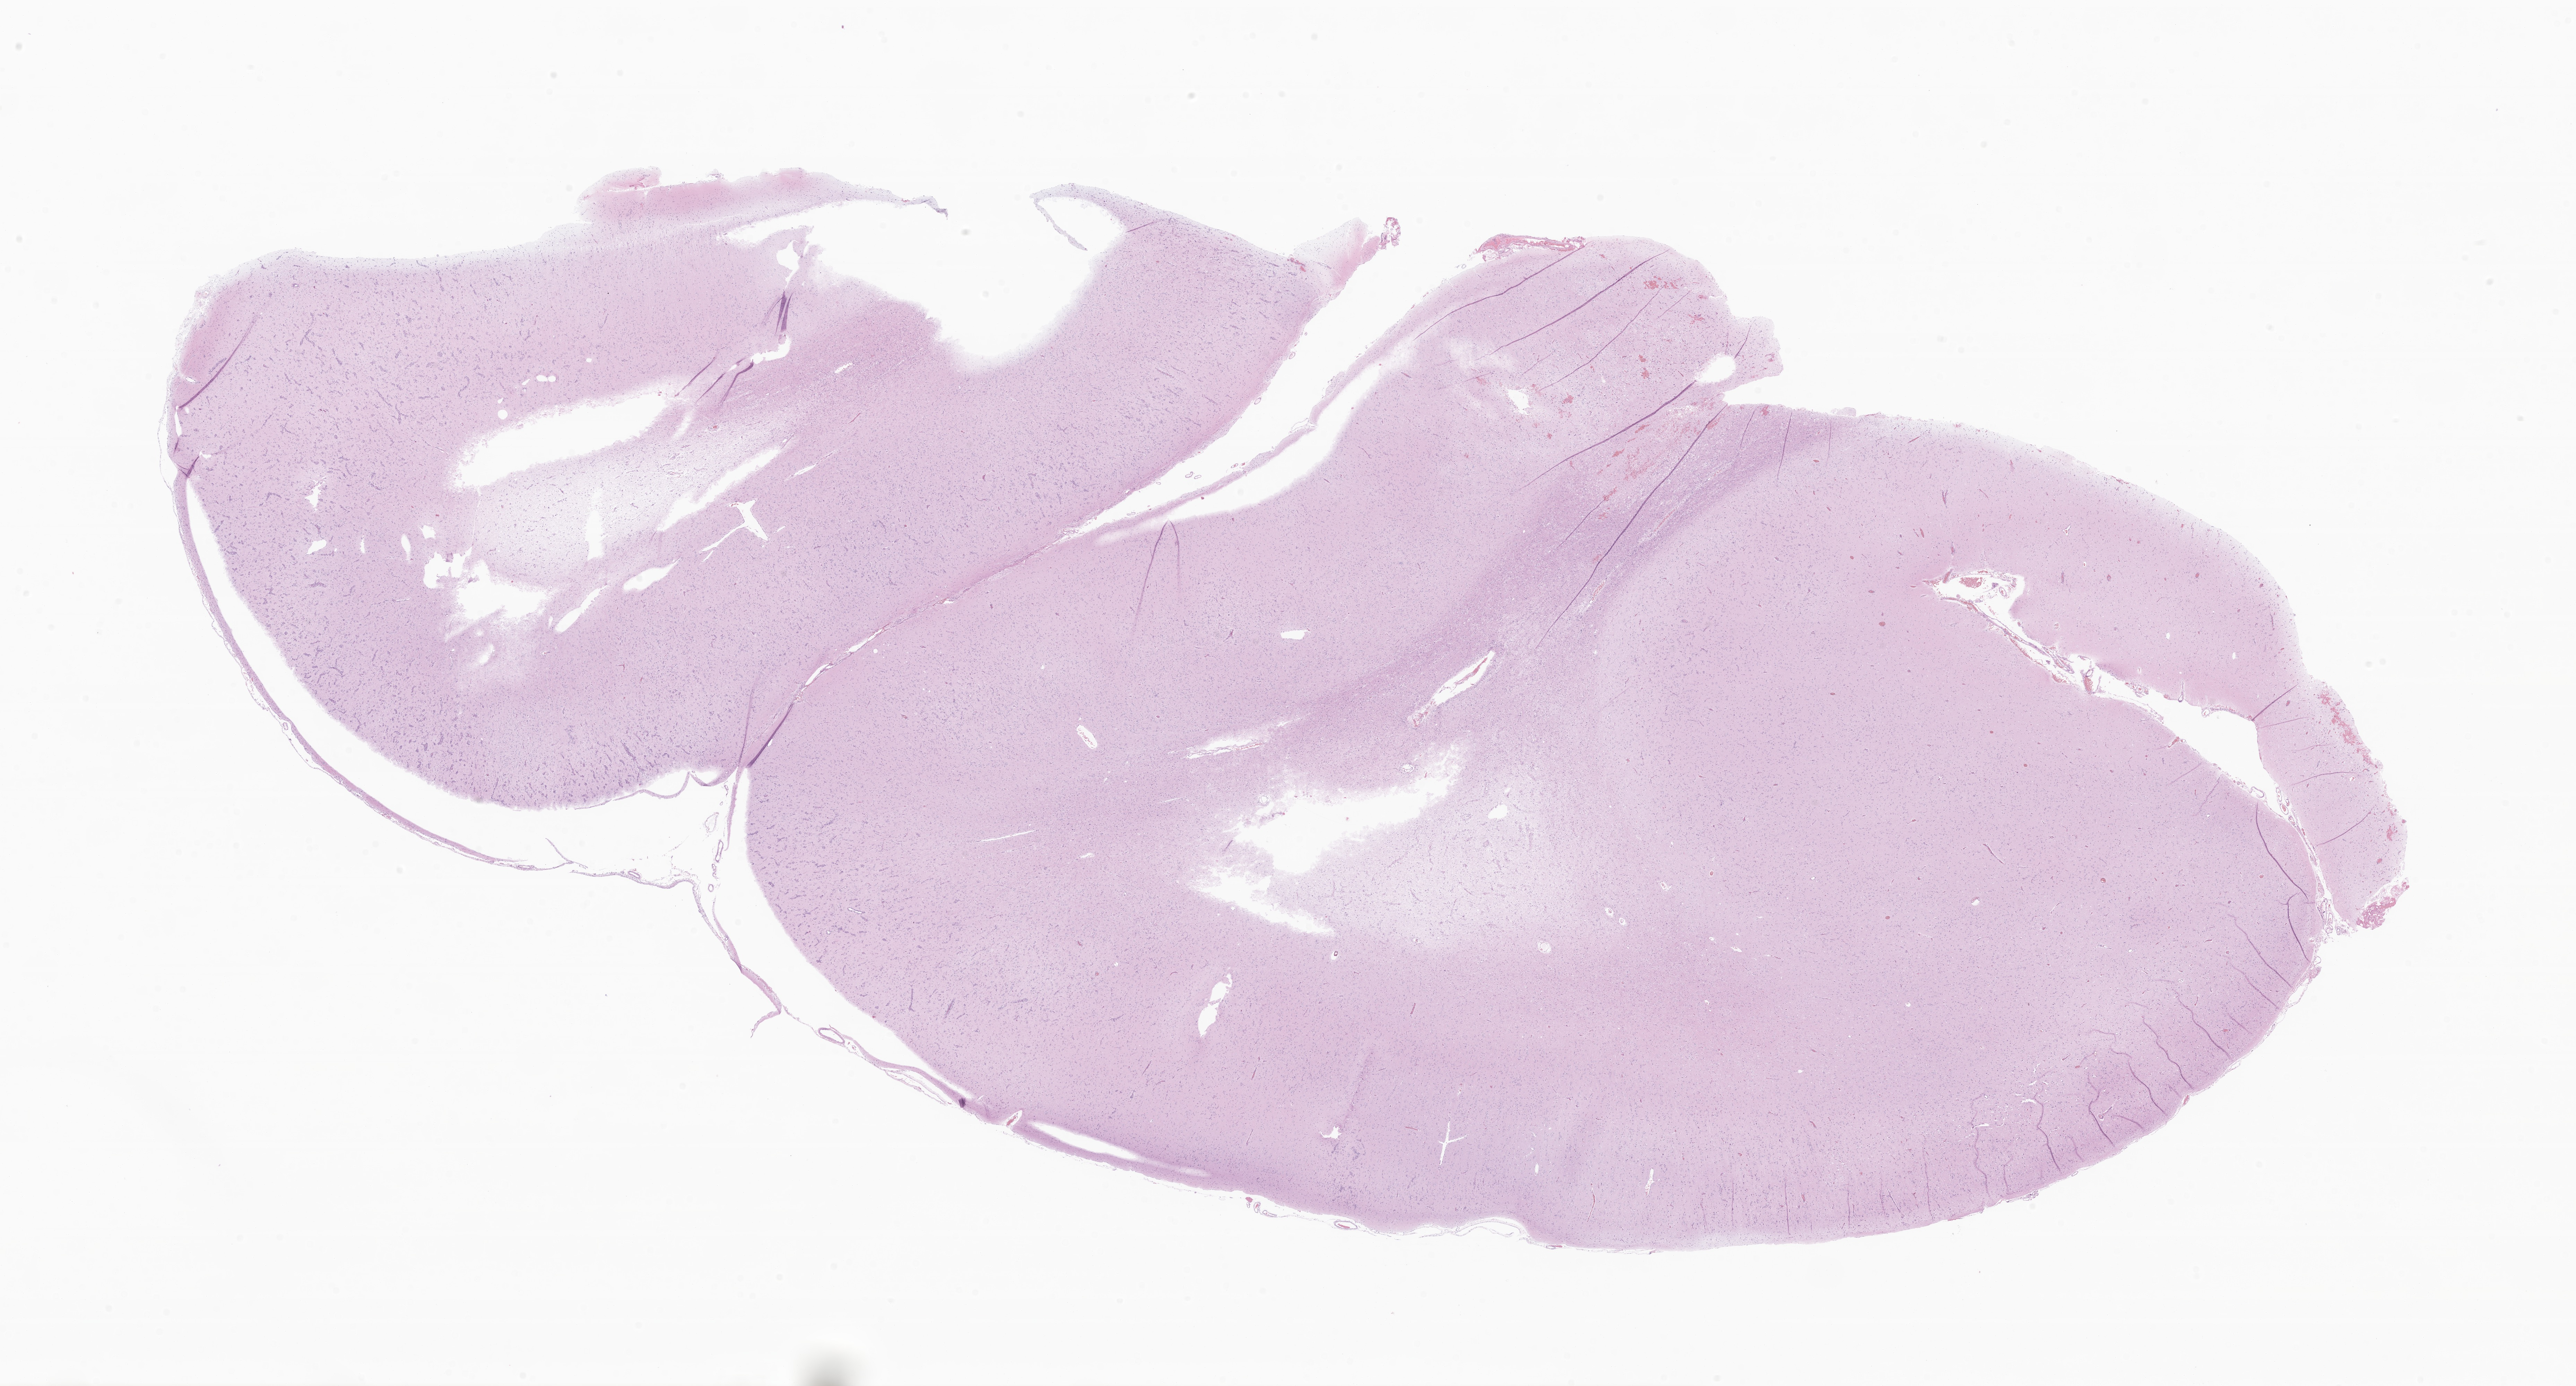
Digitized H&E-stained section of tumor tissue from the temporal lobe — a low-resolution overview of the entire scanned area, about 31.3 x 16.9 mm. FFPE section. Patient female; age 81 months.
* diagnosis (ICD-O-3 morphology term): Ganglioglioma, NOS